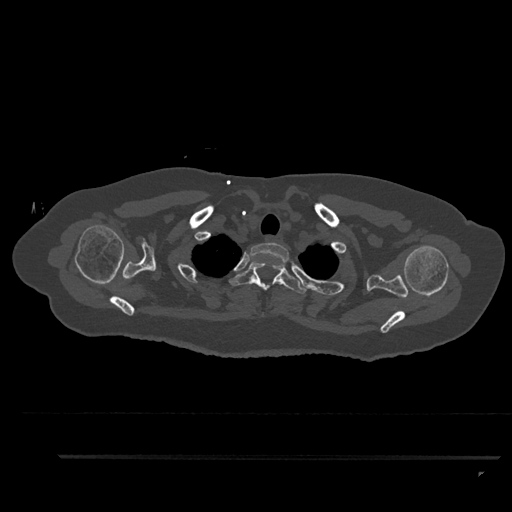
CT including the spine, one axial slice. Slice 735 of 797 in the series (ordered by position). Reconstruction kernel Br40s/3. 120 kVp. Bone window (W 1800 / L 400 HU). 0.5 mm slice thickness. 512 × 512 image matrix, field of view 408 × 408 mm. Patient: female, 44 years. Case-level facts recorded for this patient, not image findings: primary cancer: renal.
Annotated regions visible in this slice (semi-automatic segmentation, software-assisted and operator-edited):
- T1 vertebra: bounding box <249,242,289,315> (left, top, right, bottom; pixels)
- T2 vertebra: <229,262,307,294>